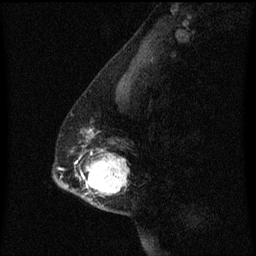
Breast MRI (dynamic contrast-enhanced), one sagittal slice; dynamic contrast-enhanced series, image 2 of 3 at this slice position (ordered by acquisition); 1.5 T; TE 4.2 ms, TR 8.4 ms; 2 mm slice thickness; 256 × 256 image matrix, field of view 200 × 200 mm. Patient: female, 40 years. From the clinical record (not read from this slice): setting: breast cancer imaged before/during neoadjuvant chemotherapy; receptor status: triple-negative.
Annotated regions visible in this slice (semi-automatic segmentation, software-assisted and operator-edited):
- analysis volume of interest (the breast-tissue region the enhancement analysis was run in; not a lesion): bounding box [x1, y1, x2, y2] px = [60, 130, 129, 213]
- tumour enhancement mask (voxels above the 70 % enhancement threshold inside the analysis volume of interest): [82, 150, 129, 195]